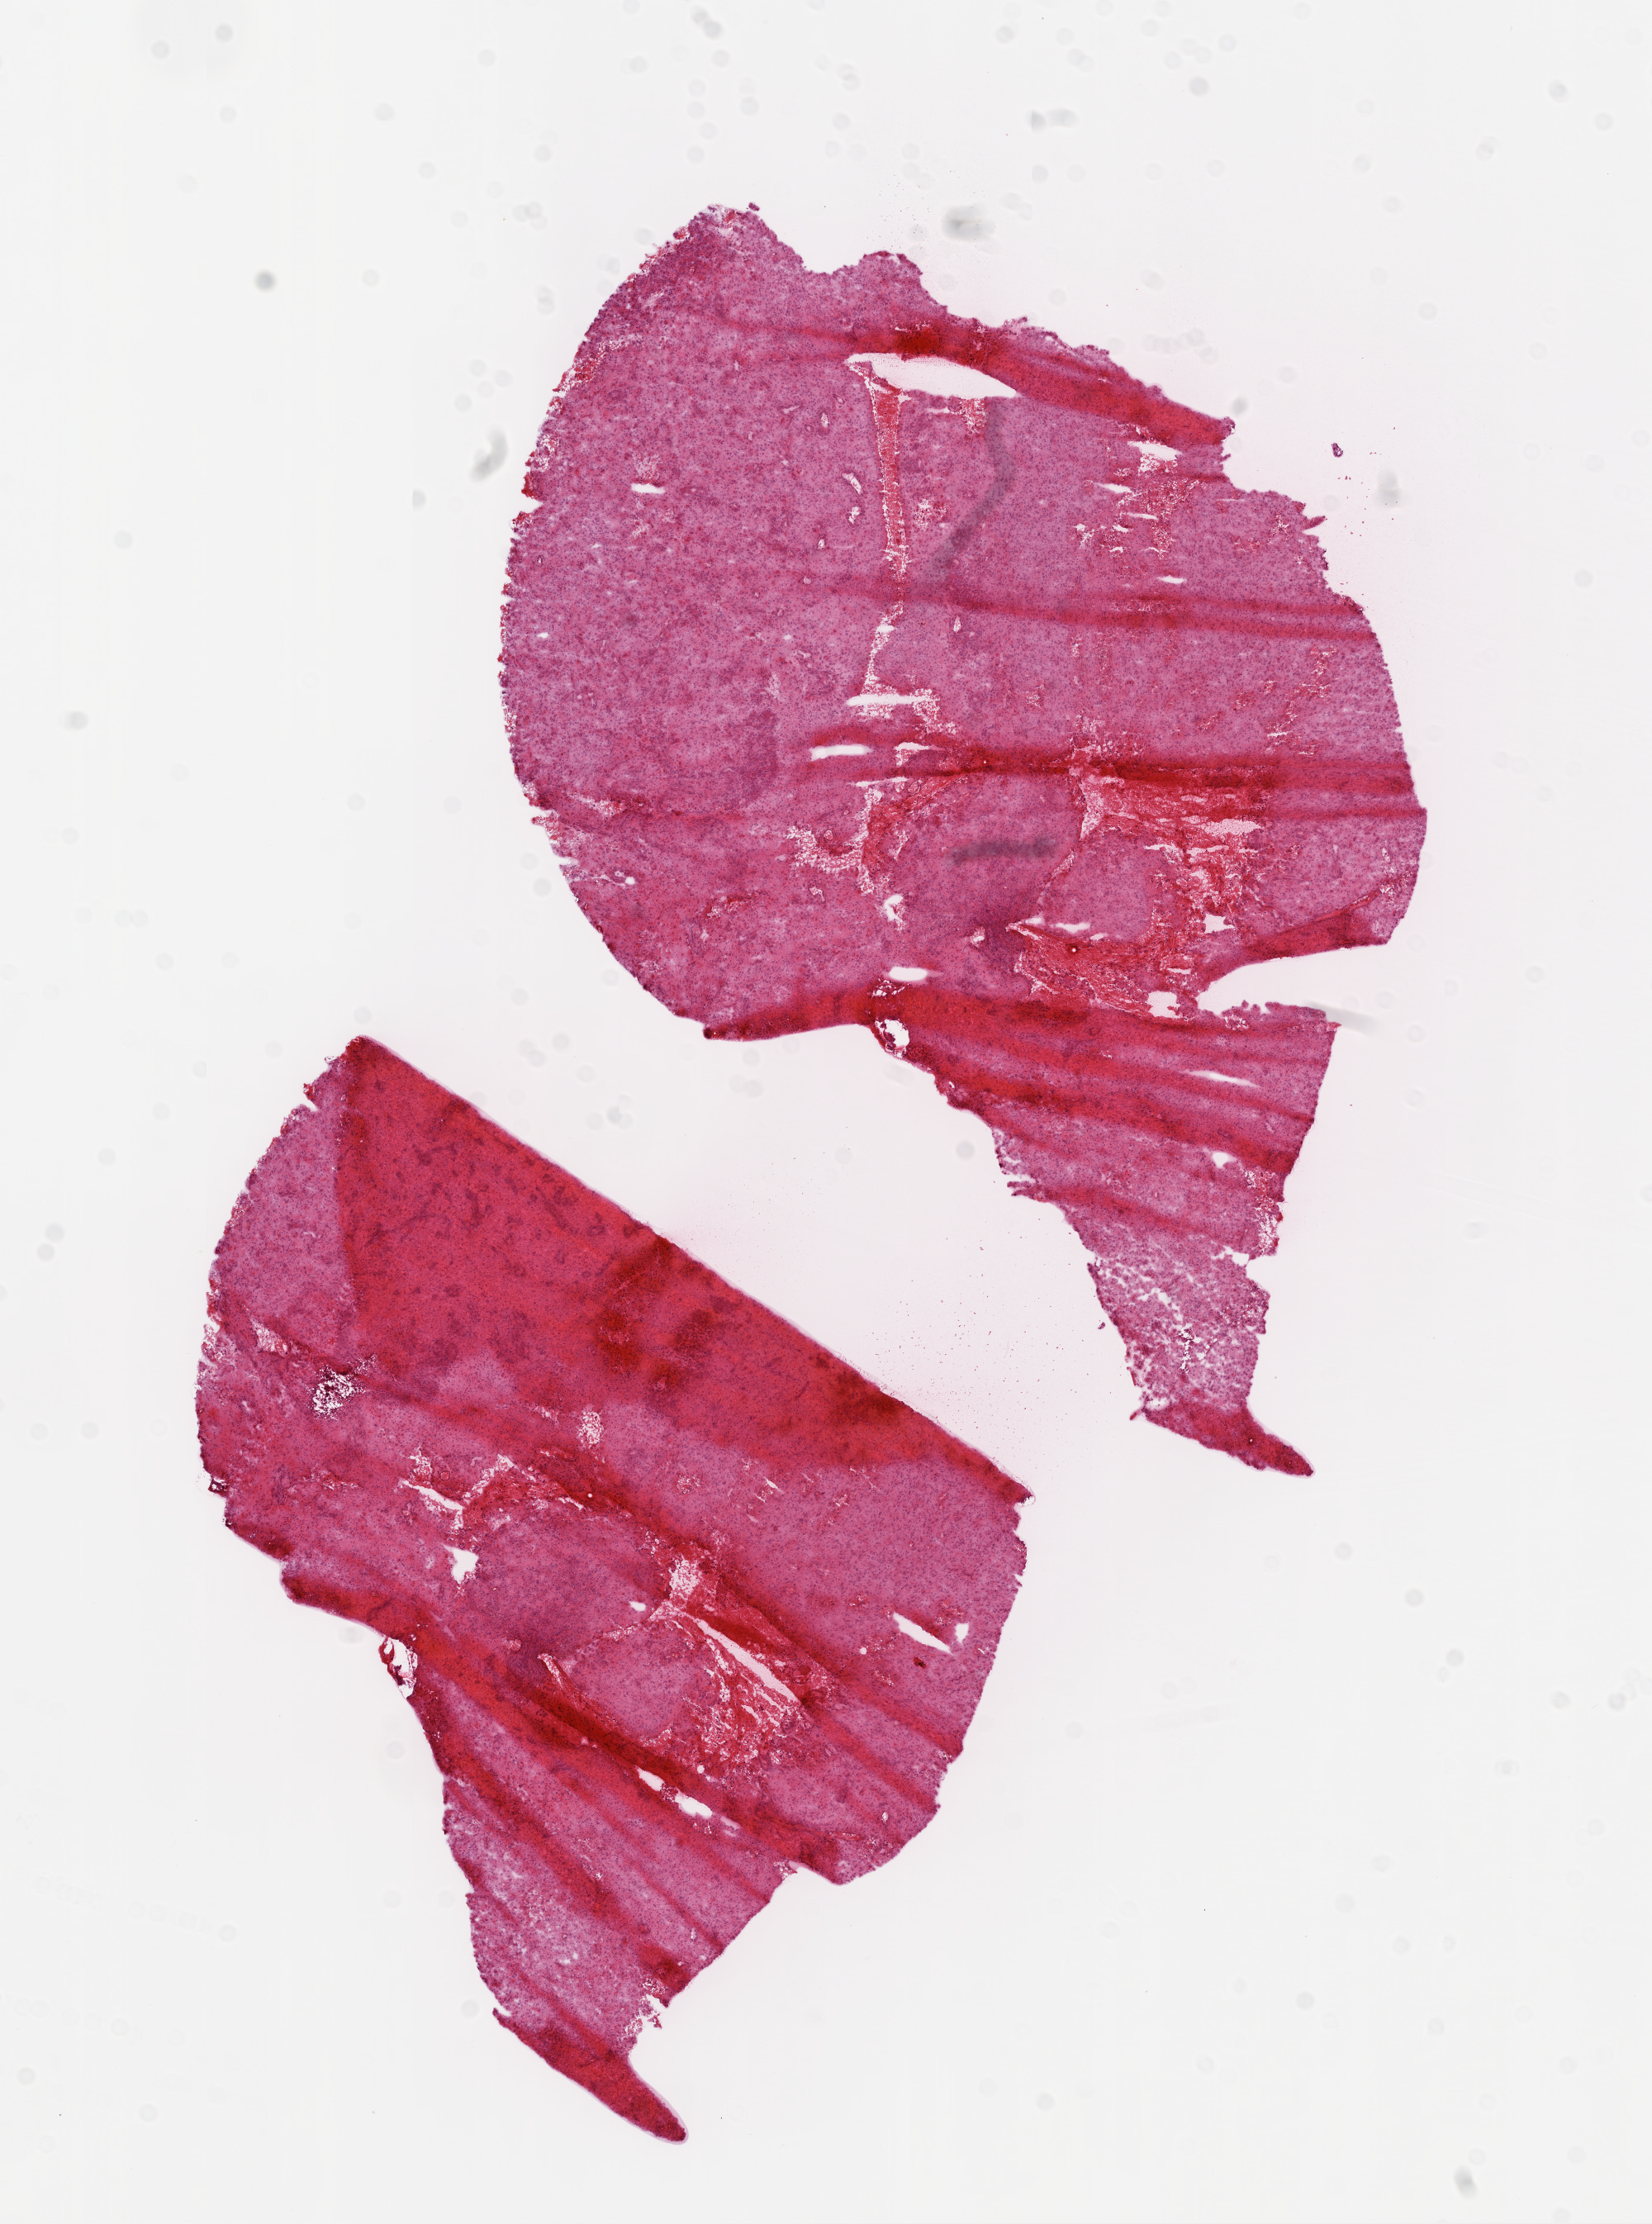
Whole-slide histology image, H&E-stained — low-resolution overview of the scanned area, about 8.0 x 10.8 mm; frozen section from the top of the tissue portion; brain, primary tumour sample. Male, age 55 years at initial diagnosis. Pathologist review of this section (percent, as recorded): tumour cells 100%, tumour nuclei 95%, normal cells 0%, stromal cells 0%, necrosis 0%.
Histologic diagnosis: Glioblastoma.